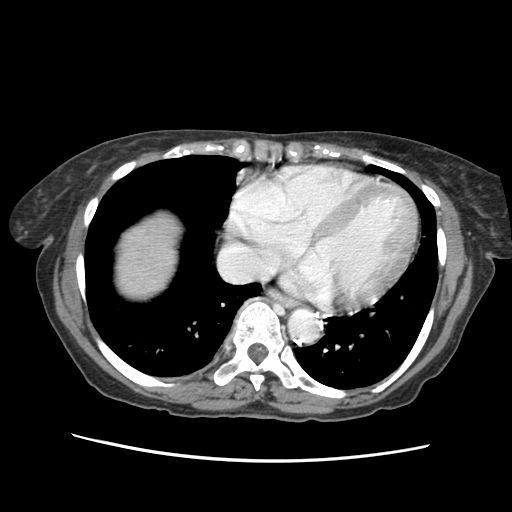
Contrast-enhanced abdominal CT (liver protocol), one axial slice; slice 58 of 63 in the series (ordered by position); reconstruction kernel STANDARD; soft-tissue window (W 400 / L 40 HU); 512 × 512 image matrix. Case-level facts recorded for this patient, not image findings: diagnosis: hepatocellular carcinoma (patient treated with transarterial chemoembolisation; whether this scan precedes or follows treatment is not stated here); TNM stage (as recorded): Stage-I; Child-Pugh class: B; tumour differentiation: well differentiated.
Outlined on this slice (semi-automatically segmented with operator editing):
- liver parenchyma outside the tumour (the mass and vessels are separate outlines, so this box may not span the whole liver): bounding box [x1, y1, x2, y2] px = [120, 218, 172, 292]